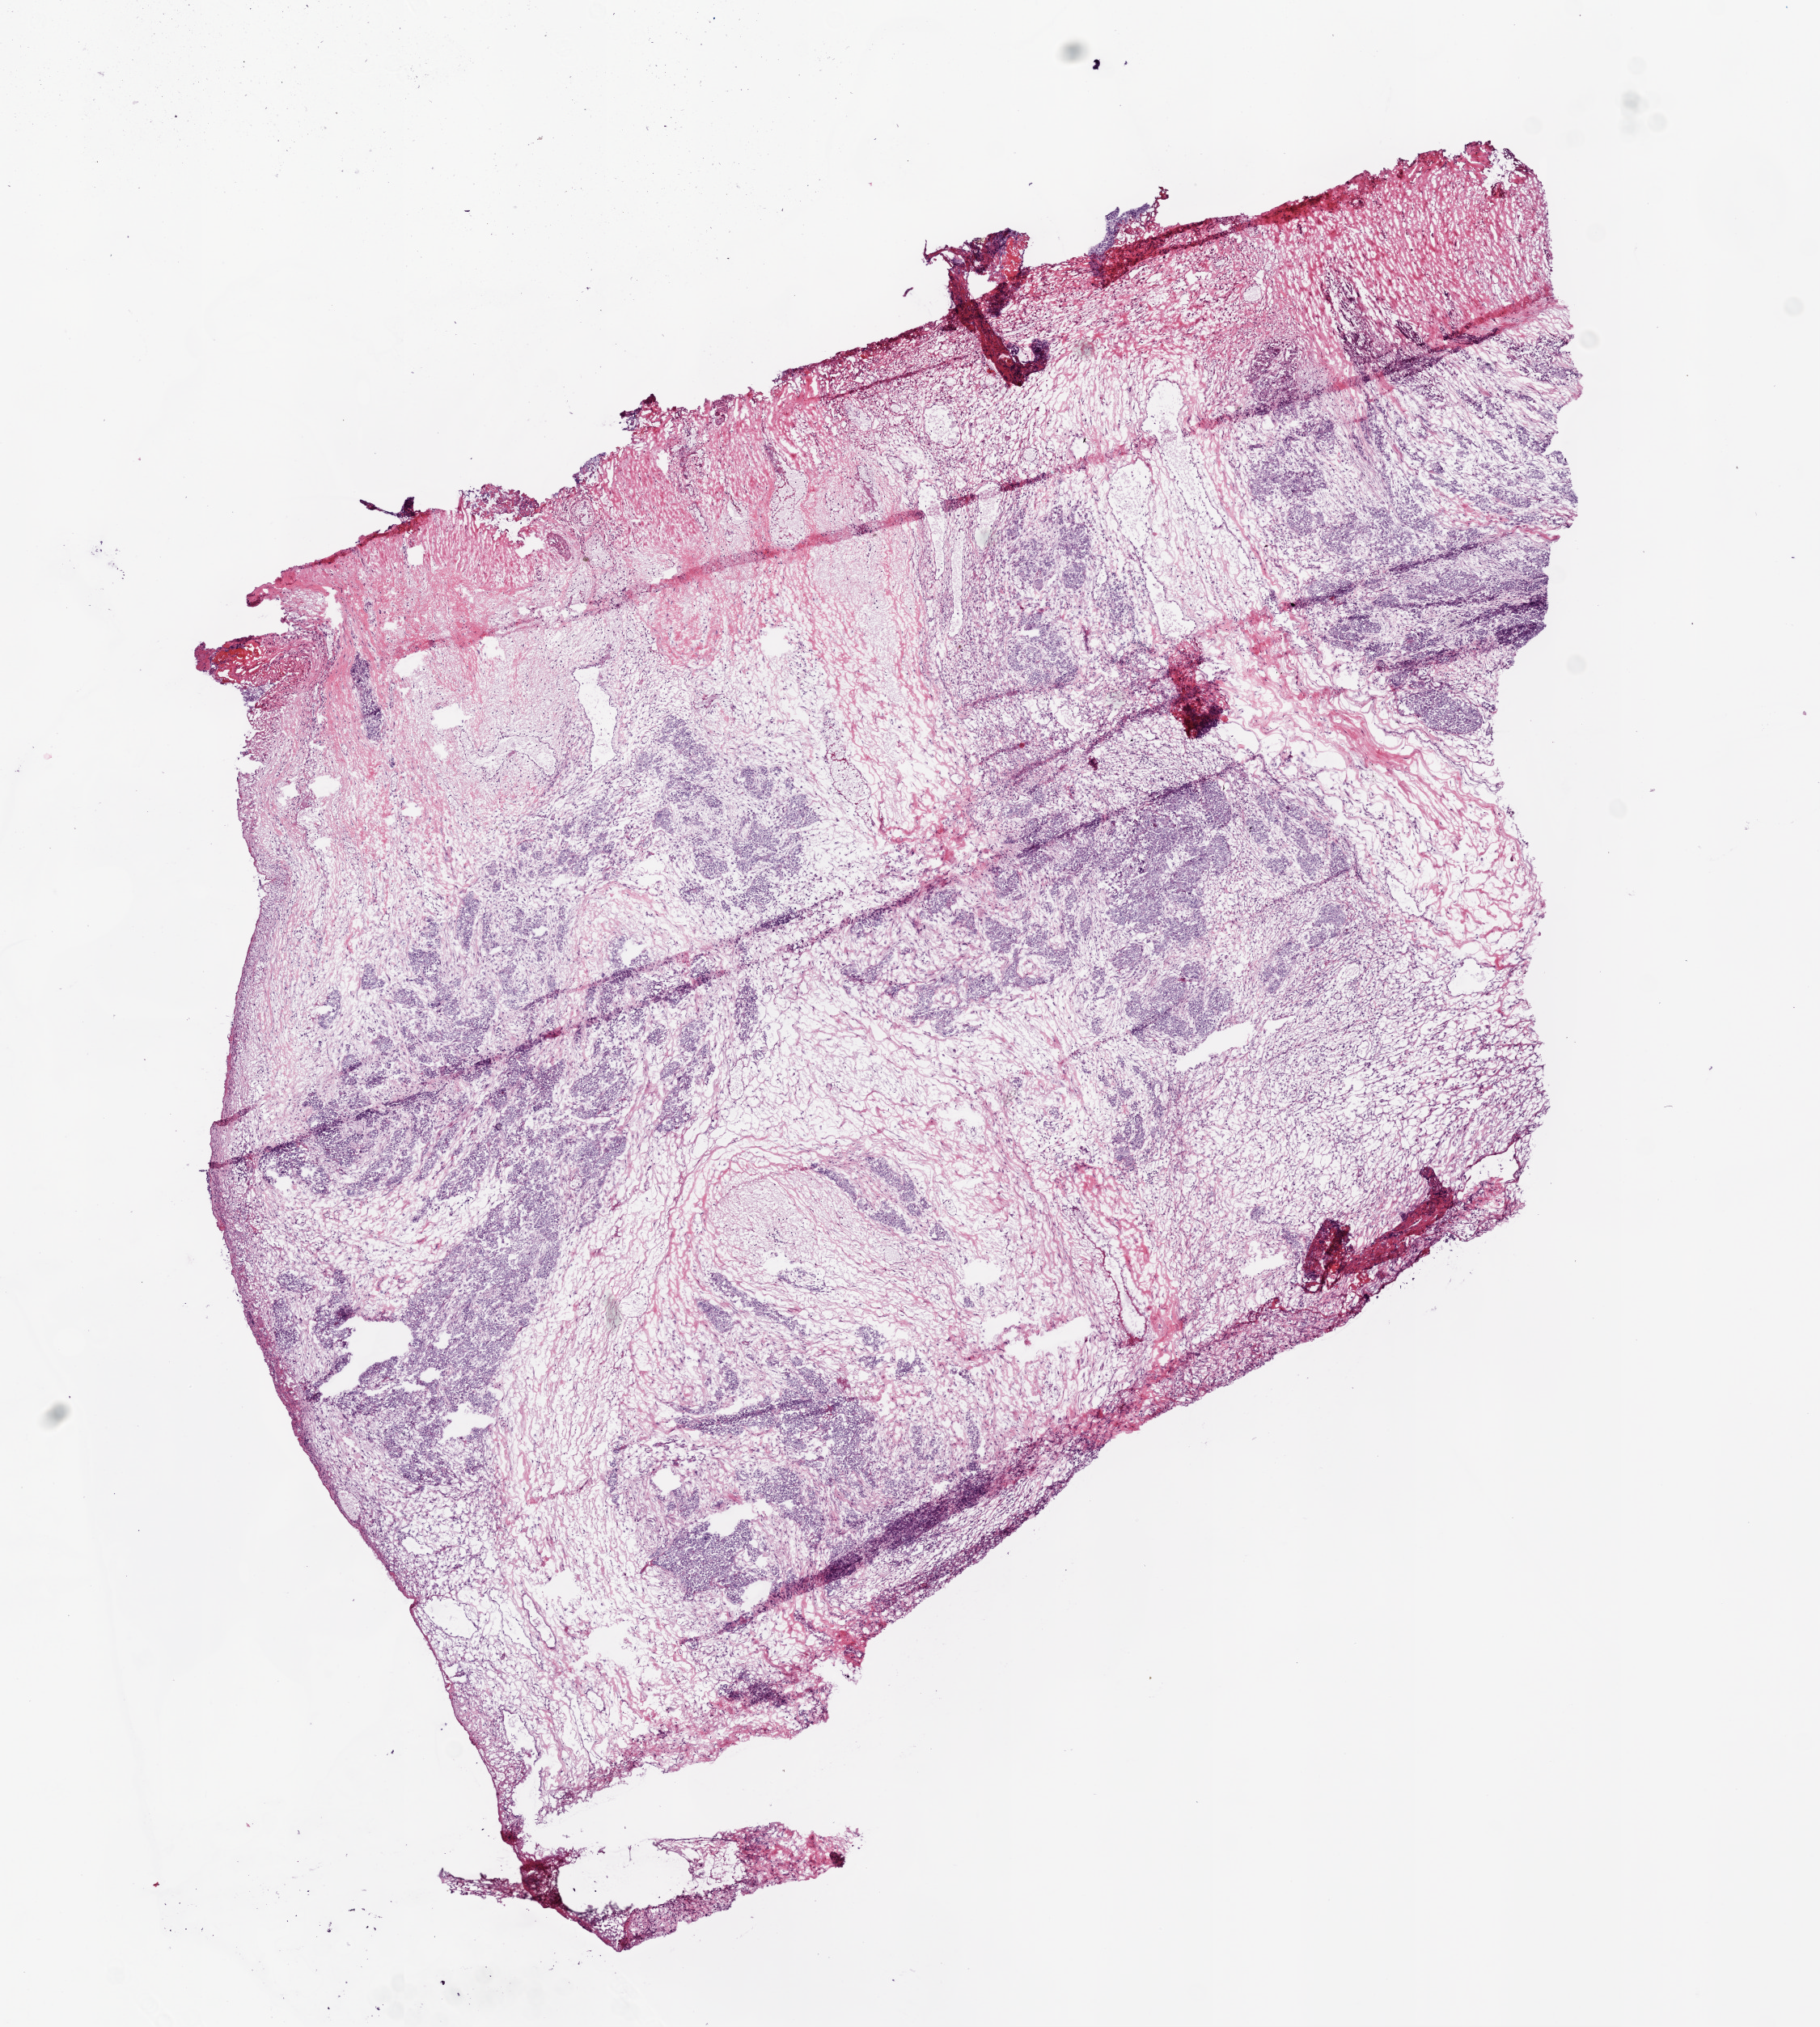
Digitized H&E-stained tissue section (whole slide), low-resolution overview of the scanned area, about 9.0 x 10.1 mm (slide scanned at 20x); frozen section from the bottom of the tissue portion; ovary, primary tumour sample. Patient: female, age at initial diagnosis 60 years. Histologic grade: G3 (poorly differentiated). Pathologist review of this section (percent, as recorded): tumour cells 30%, tumour nuclei 85%, normal cells 0%, stromal cells 68%, necrosis 2%.
- laterality: bilateral
- FIGO stage: IIIC
- pathologic diagnosis: Serous cystadenocarcinoma, NOS